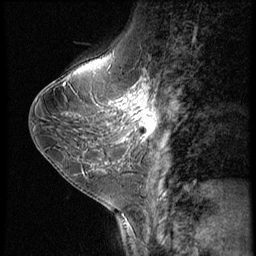
Breast MRI (dynamic contrast-enhanced), one sagittal slice. Position 22 of 56 along the scan axis. Dynamic contrast-enhanced series, image 2 of 3 at this slice position (ordered by acquisition). 1.5 T. TE 4.2 ms, TR 9 ms. 2.5 mm slice thickness. 256 × 256 image matrix, field of view 180 × 180 mm. Patient: female, 38 years. Case-level facts recorded for this patient, not image findings: setting: breast cancer imaged before/during neoadjuvant chemotherapy; receptor status: triple-negative.
Annotated regions visible in this slice (semi-automatically segmented with operator editing):
- analysis volume of interest (the breast-tissue region the enhancement analysis was run in; not a lesion): box from (x=107, y=95) to (x=163, y=149) px
- tumour enhancement mask (voxels above the 140 % enhancement threshold inside the analysis volume of interest): (x=112, y=95)–(x=157, y=139)